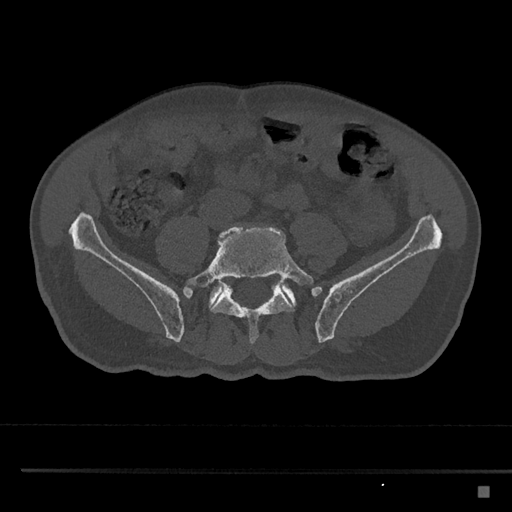
CT including the spine, one axial slice; reconstruction kernel Br40s/3; bone window (W 1800 / L 400 HU); 512 × 512 image matrix. Patient: male, 59 years. From the clinical record (not read from this slice): primary cancer: prostate.
Outlined on this slice (semi-automatic segmentation, software-assisted and operator-edited):
- L5 vertebra: bounding box [x1, y1, x2, y2] px = [183, 225, 314, 344]